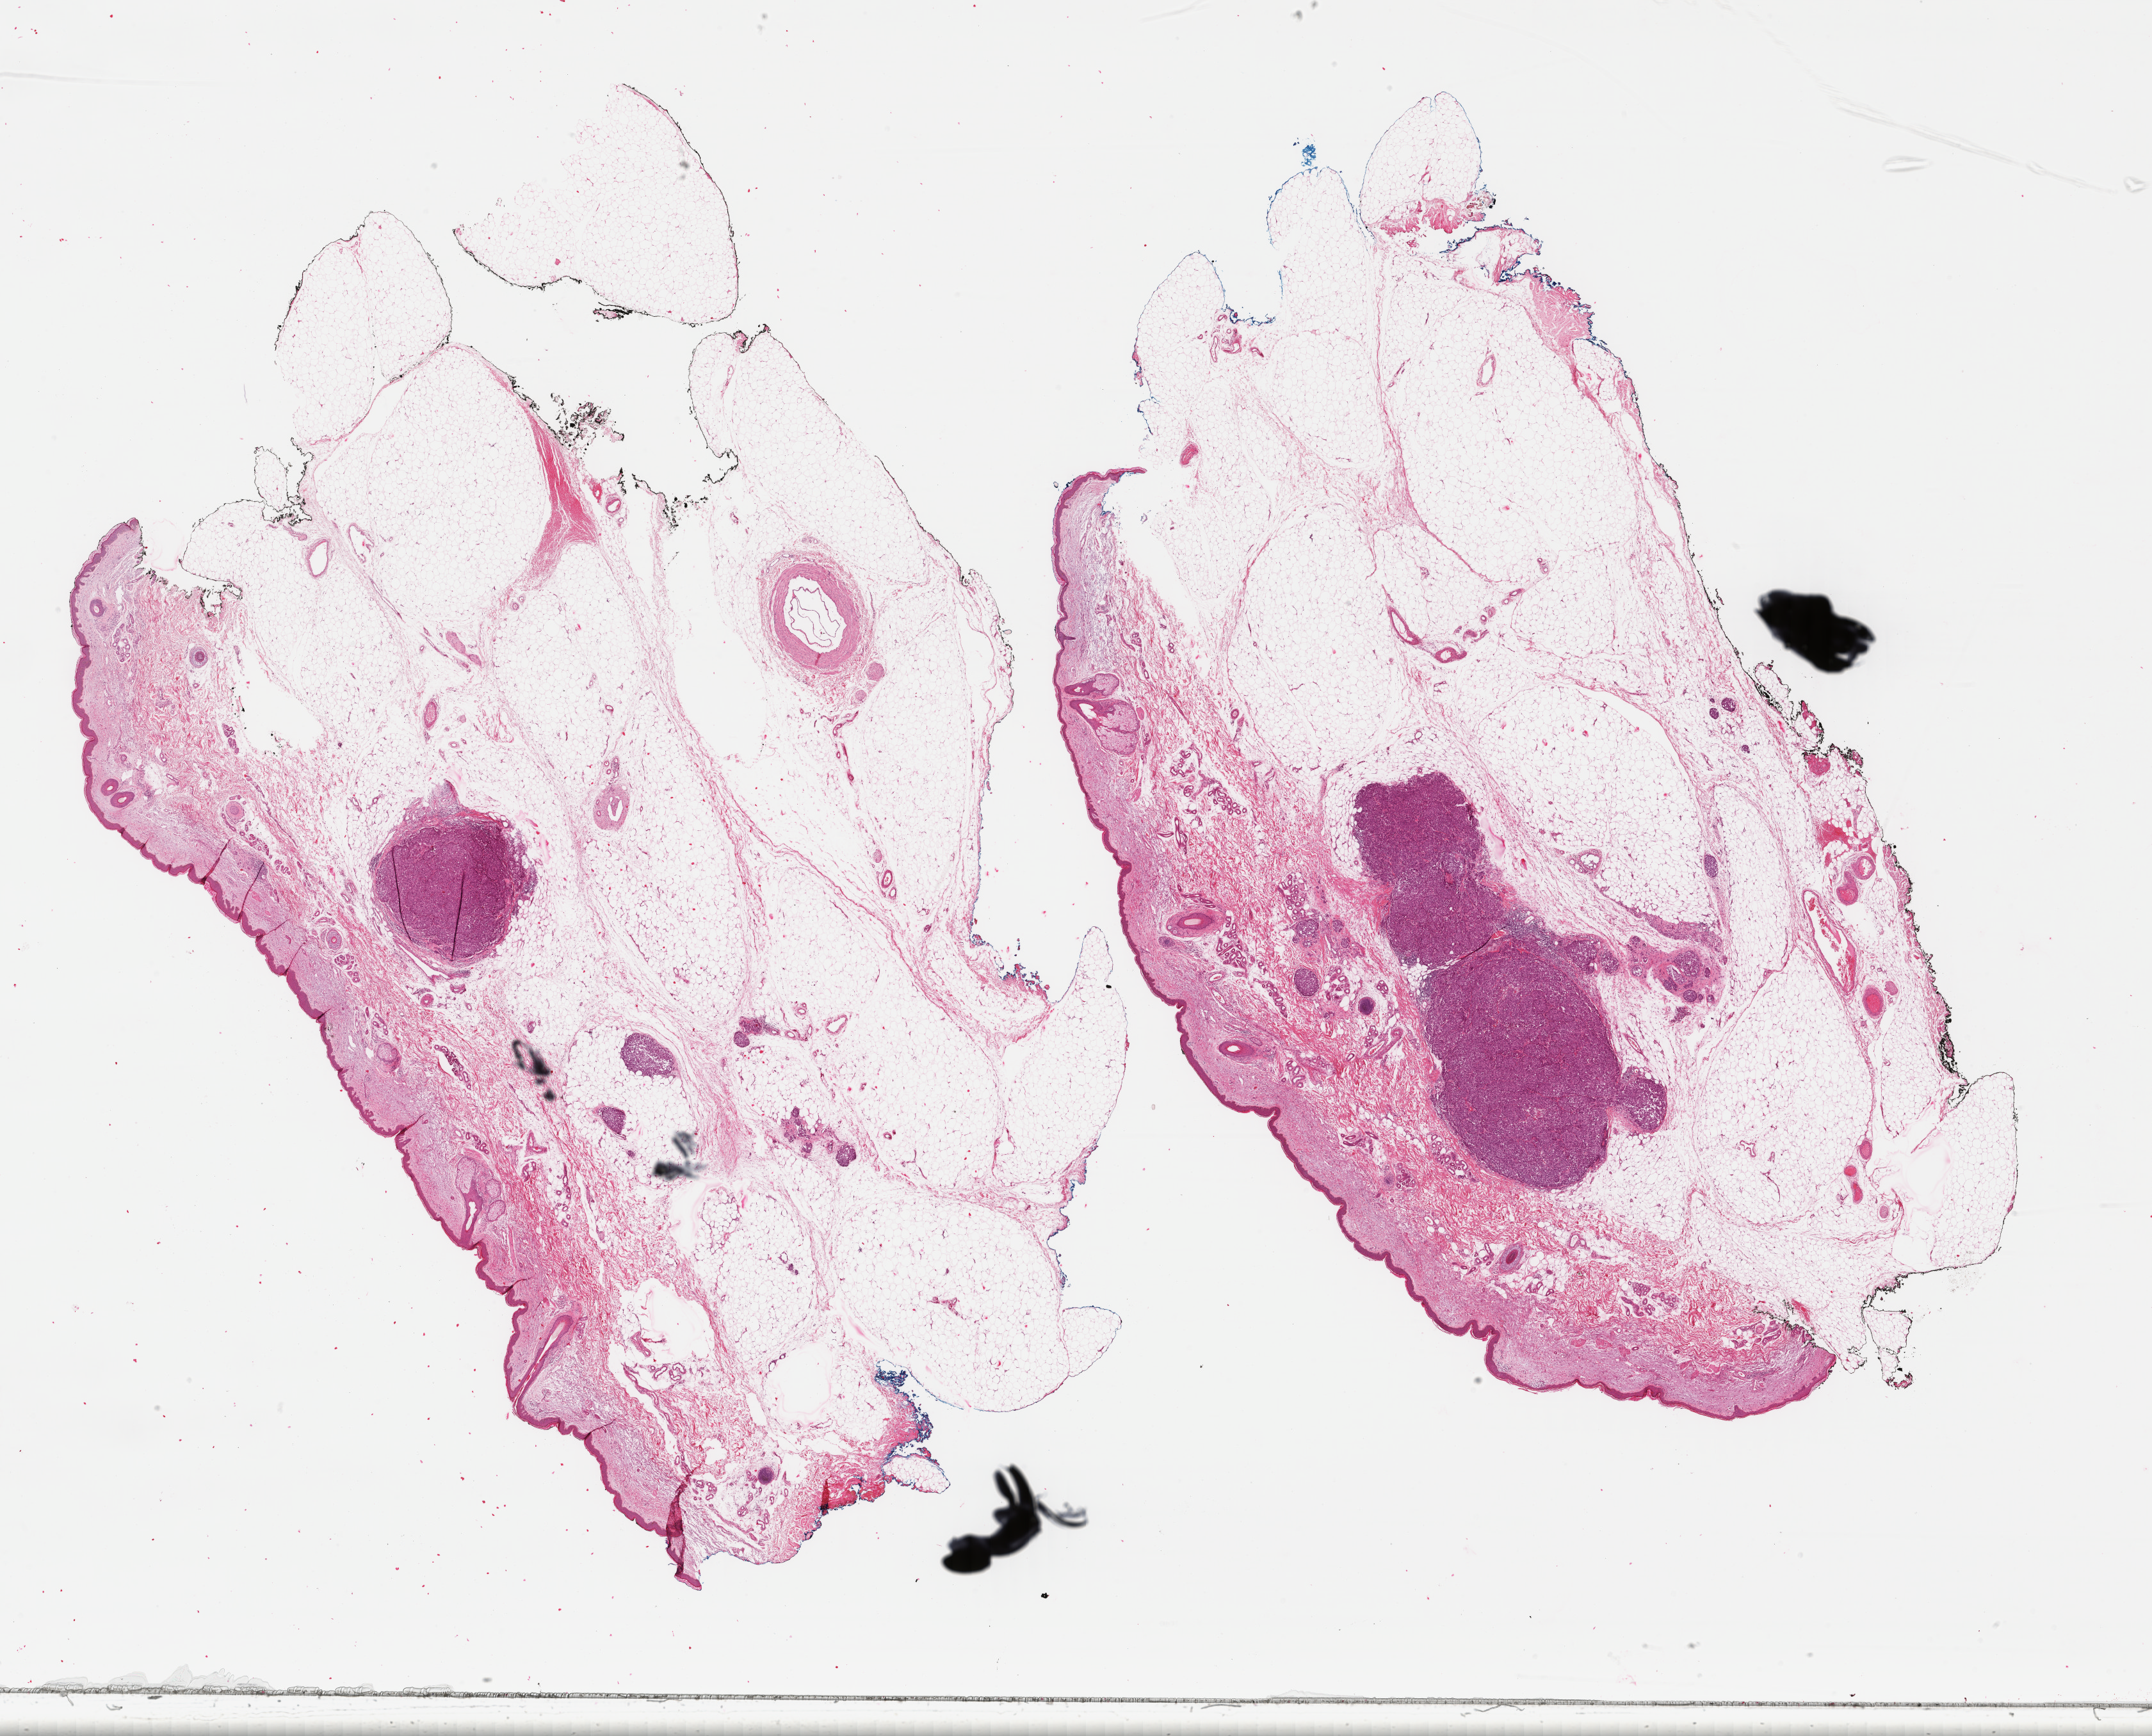
Digitized H&E-stained tissue section (whole slide), shown as a low-resolution overview of the whole scanned area (about 26.7 x 21.5 mm, slide scanned at 40x); formalin-fixed paraffin-embedded (FFPE) diagnostic section; primary tumour sample from the skin. Male patient; age at initial diagnosis 78 years.
- pathologic diagnosis: Malignant melanoma, NOS